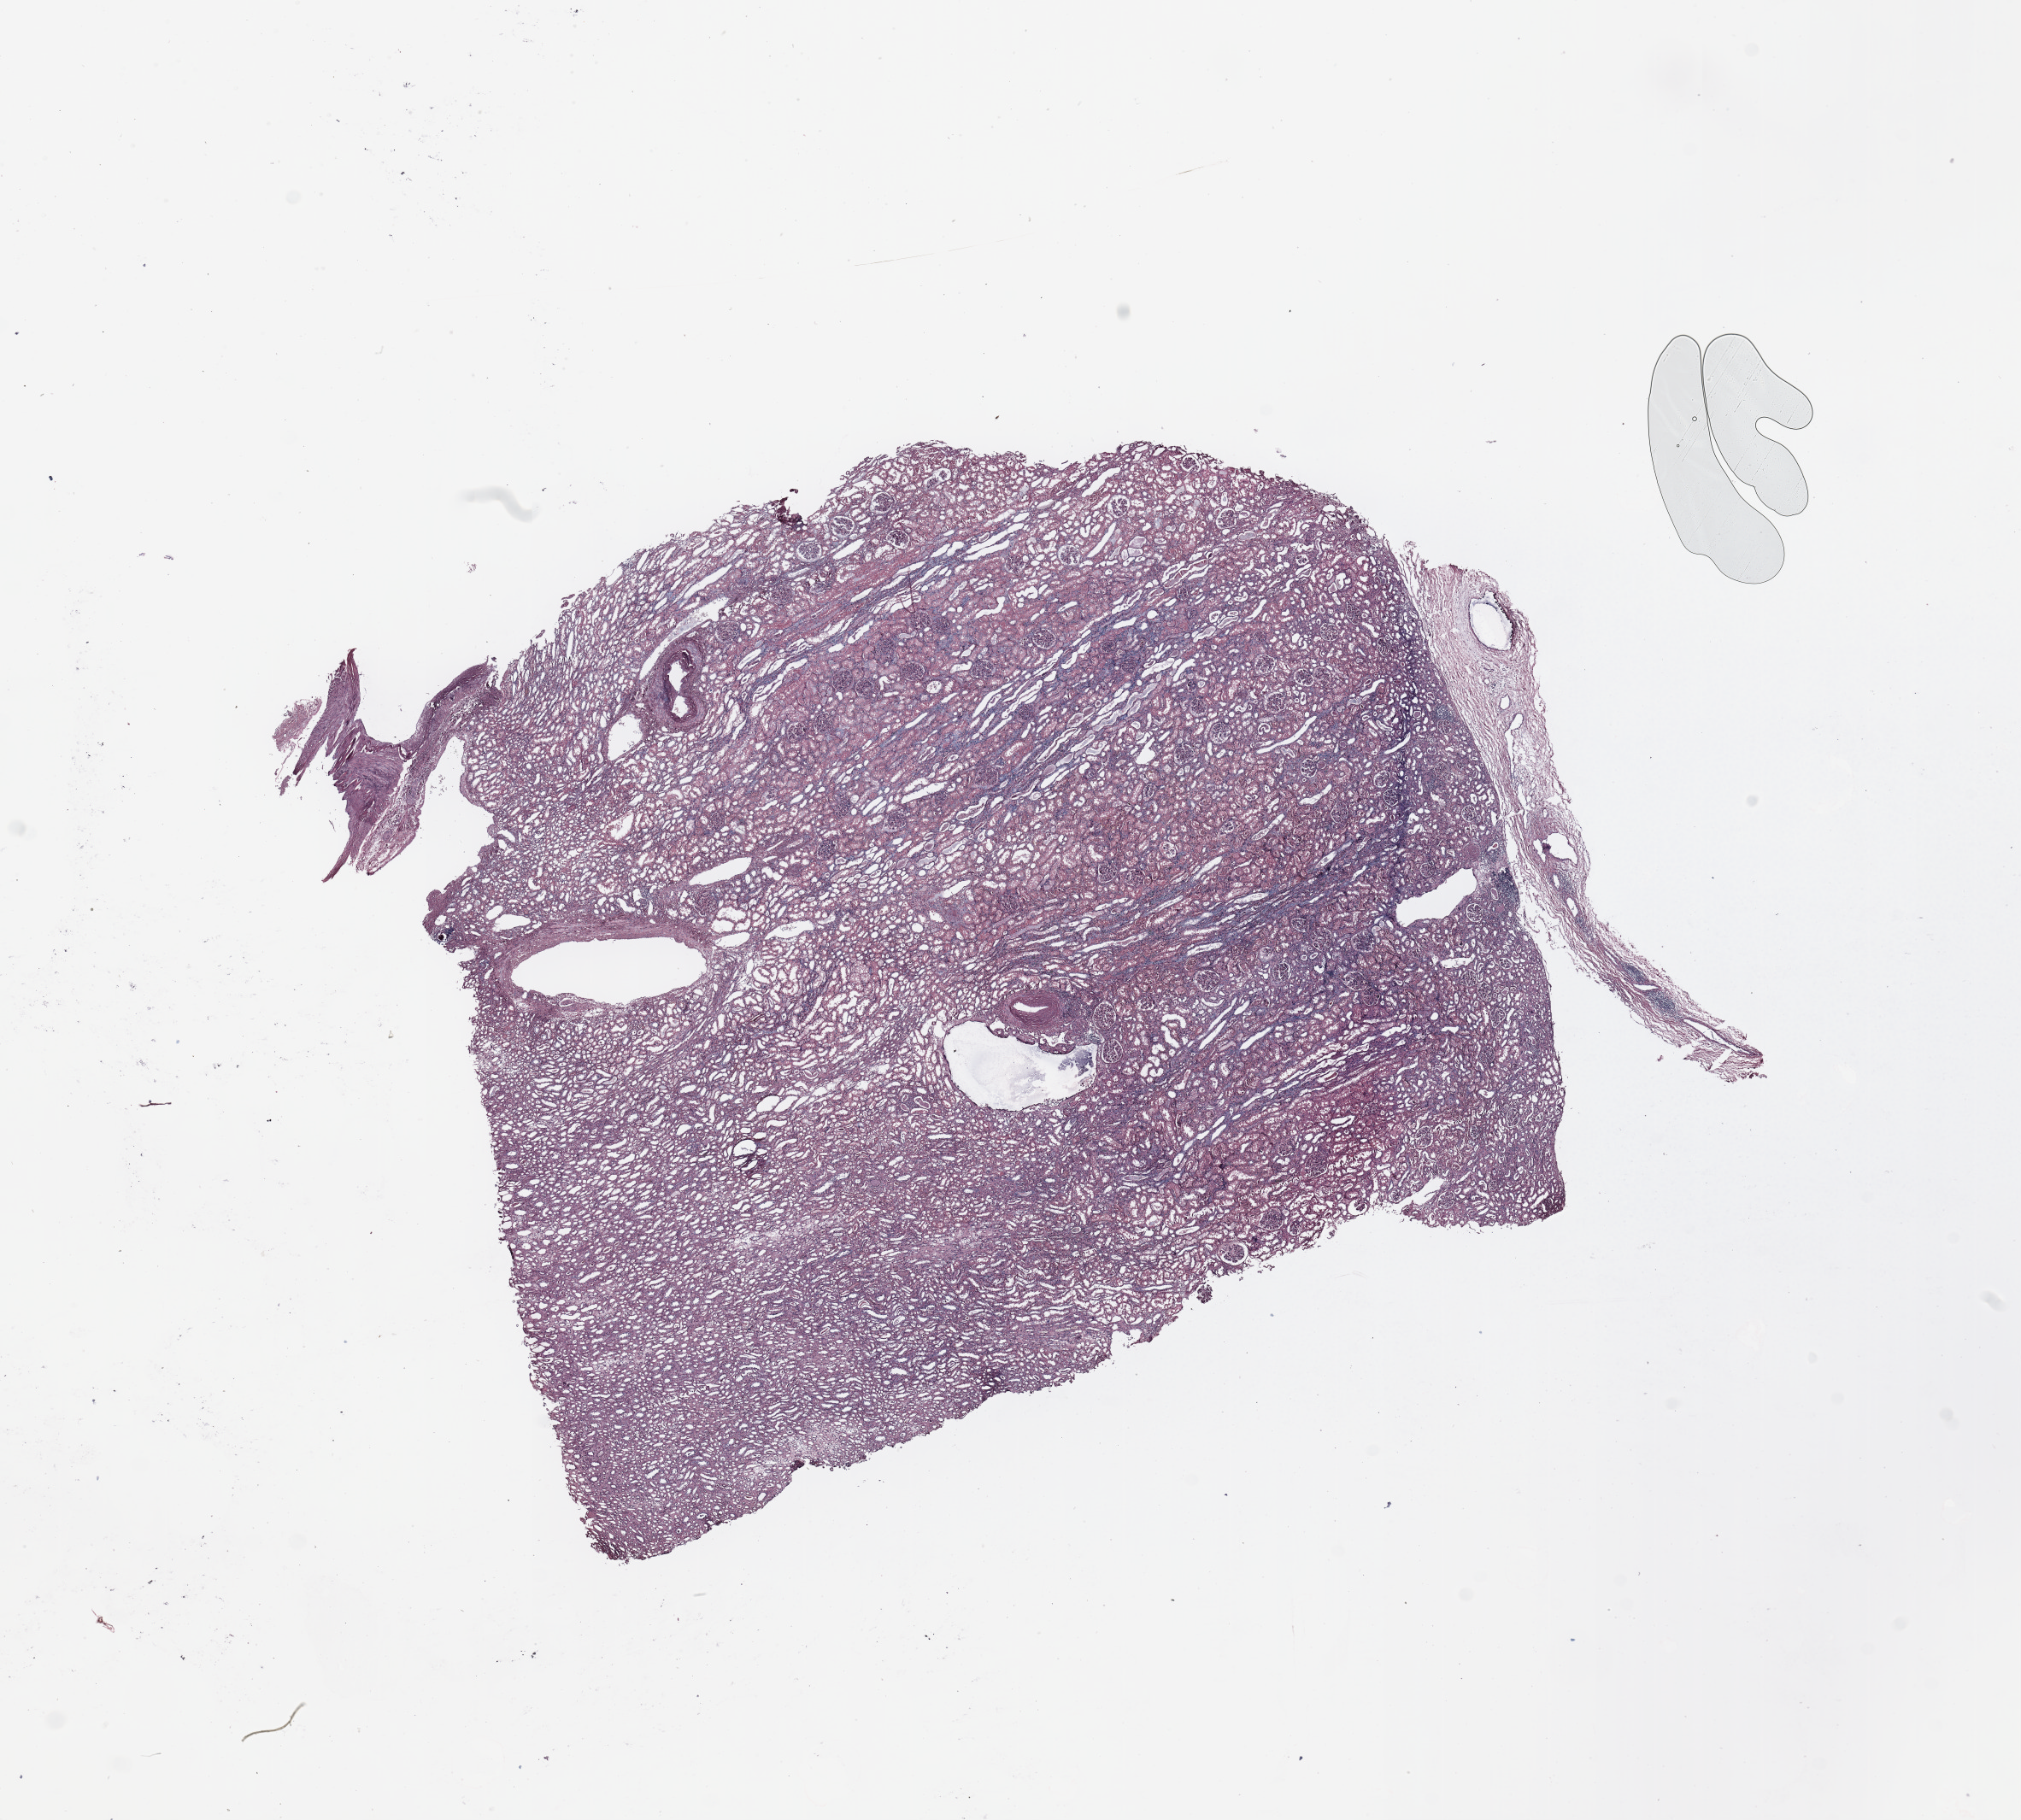
Whole-slide histology image, H&E — low-resolution overview of the scanned area, about 18.7 x 16.8 mm (slide scanned at 20x); normal (non-tumour) tissue sample, sampled site: kidney. 56-year-old female patient.
This section: normal (non-tumour) tissue from the same patient. Patient diagnosis: Renal cell carcinoma, NOS.